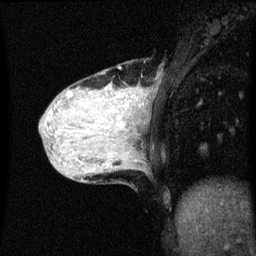
Breast MRI (dynamic contrast-enhanced), one sagittal slice; position 17 of 60 along the scan axis; dynamic contrast-enhanced series, image 2 of 3 at this slice position (ordered by acquisition); 1.5 T; TE 4.2 ms, TR 8.4 ms; 2 mm slice thickness; 256 × 256 image matrix, field of view 200 × 200 mm. Female patient, age 36 years.
Annotated regions visible in this slice (semi-automatically segmented with operator editing):
- analysis volume of interest (the breast-tissue region the enhancement analysis was run in; not a lesion): bounding box (x1, y1, x2, y2) in pixels: (48, 70, 147, 151)
- tumour enhancement mask (voxels above the 70 % enhancement threshold inside the analysis volume of interest): (58, 98, 139, 125)